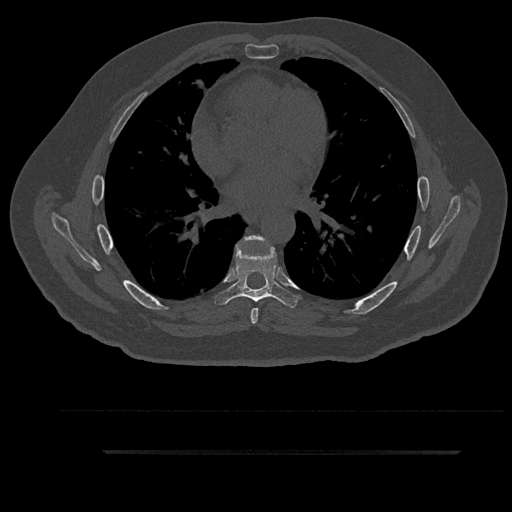
CT including the spine, one axial slice; slice 541 of 797 in the series (ordered by position); bone window (W 1800 / L 400 HU); 0.5 mm slice thickness; 512 × 512 image matrix. Male patient, age 63 years. From the clinical record (not read from this slice): primary cancer: renal; vertebrae with lytic lesions (as recorded): T8.
Outlined on this slice (semi-automatically segmented with operator editing):
- T6 vertebra: bounding box <245,236,266,324> (left, top, right, bottom; pixels)
- T7 vertebra: <214,240,299,308>